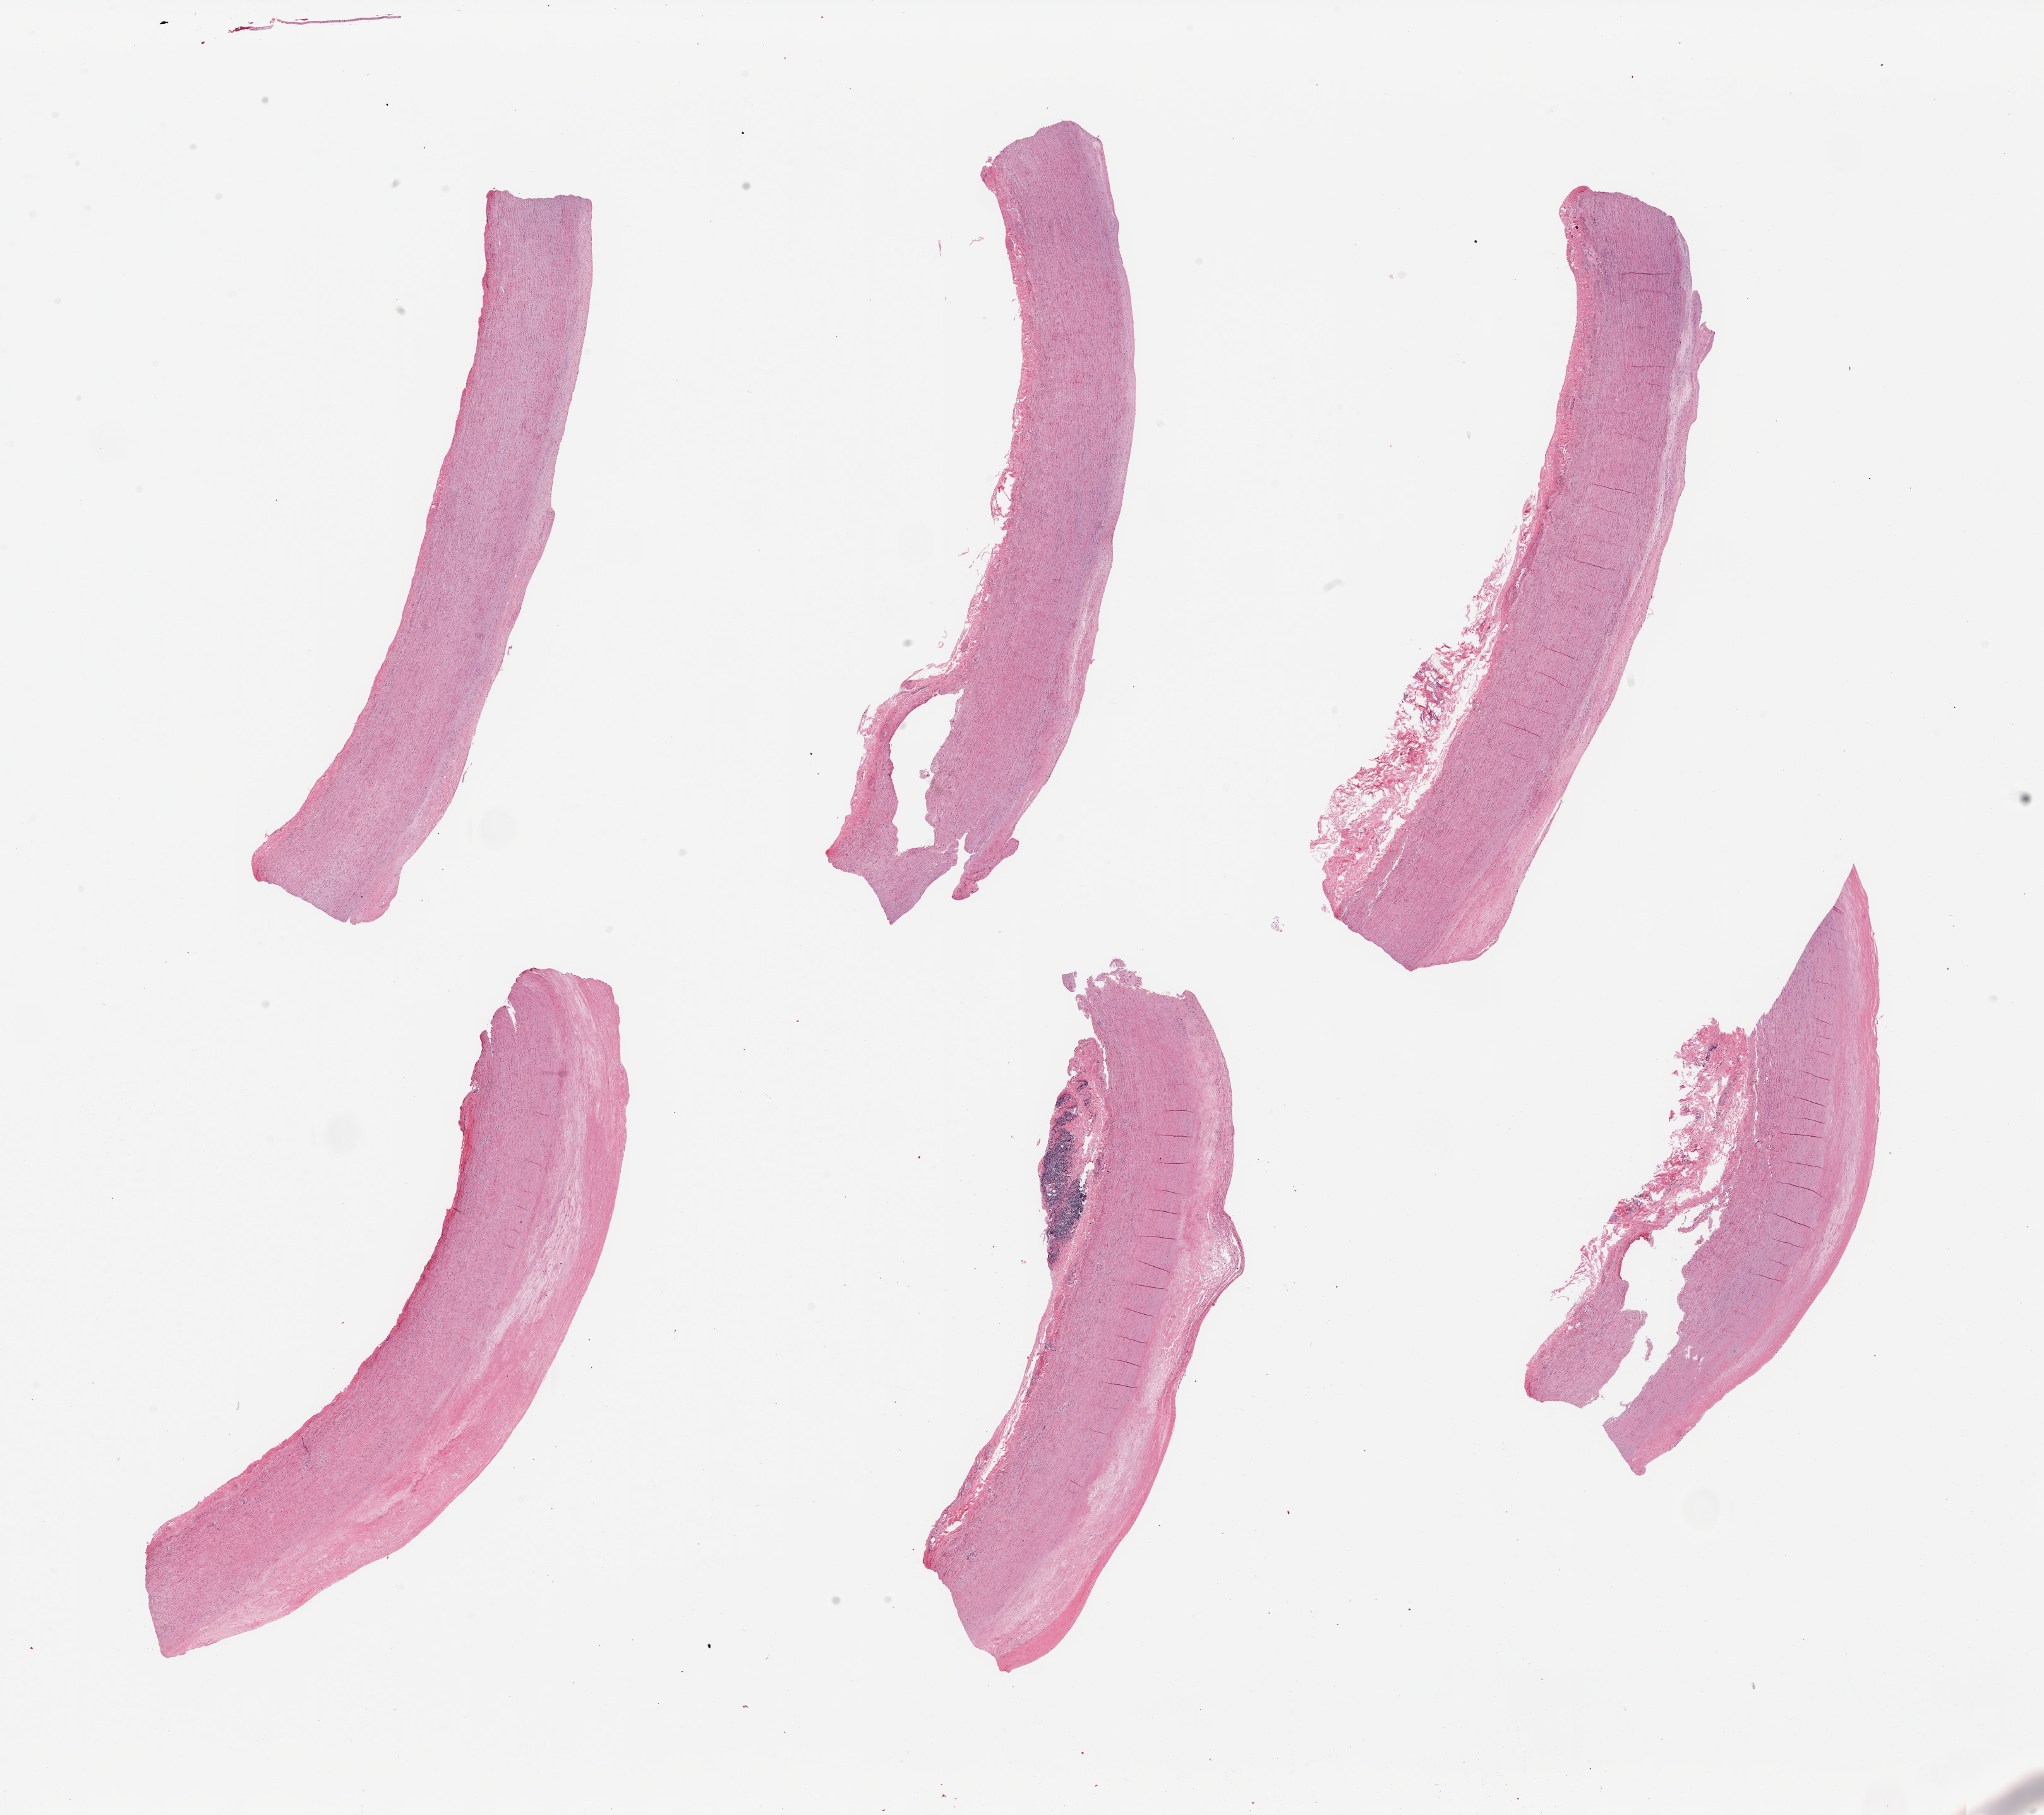
Digitized hematoxylin and eosin (H&E)-stained section — whole scanned area (about 25.6 x 22.7 mm, from a 20x scan) shown as a low-resolution overview; PAXgene-fixed, paraffin-embedded tissue; sampled site (target tissue): aorta; tissue donor sample. Donor: male.
Pathologist's review note for this sample: 6 pieces; severe atherosclerosis, collection of lymphocytes within adventitia, two pieces show defects within the wall (? secondary to processing).